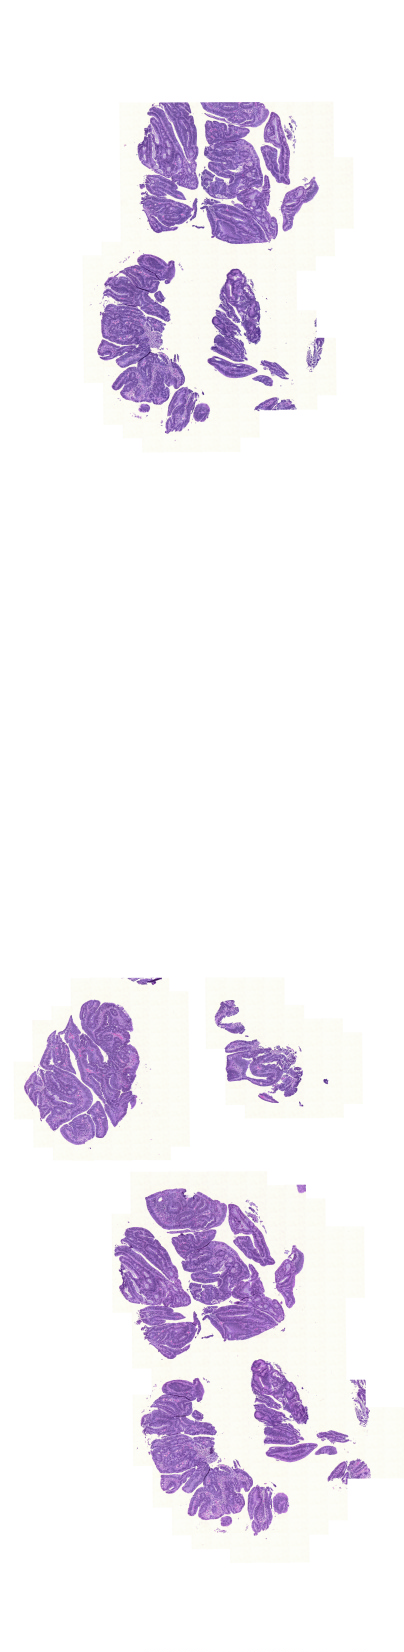
Digitized Hematoxylin and eosin (H&E) stained tissue section (whole slide) — whole scanned area (about 6.0 x 24.6 mm, from a 20x scan) shown as a low-resolution overview. FFPE section. Primary tumour sample from the colon. Male, age 76 years at initial diagnosis.
- histologic diagnosis: Adenocarcinoma, NOS (sigmoid colon)
- AJCC pathologic stage: I (6th edition)
- lymph nodes positive (case pathology): 0 of 36 examined